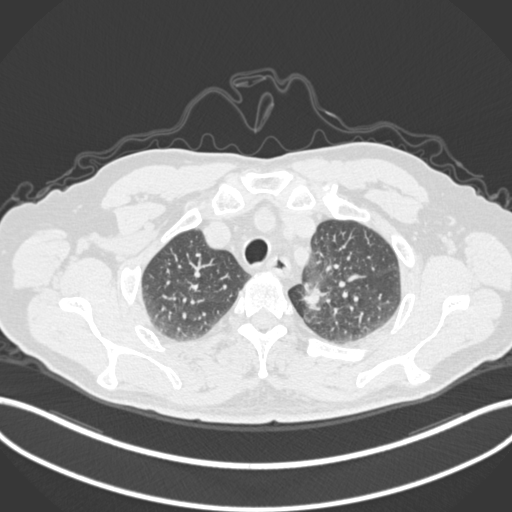
Chest CT, one axial slice; position 269 of 306 along the scan axis; reconstruction kernel B30f; 120 kVp; lung window (W 1500 / L -600 HU); 1 mm slice thickness; 512 × 512 image matrix, field of view 400 × 400 mm. Patient: male, 64 years. Case-level facts recorded for this patient, not image findings: clinical TNM (as recorded): T1c N0 M0.
Structures marked on this image (rectangle marked by the reading radiologist):
- lung tumour (recorded histology: adenocarcinoma): bounding box <300,277,332,314> (left, top, right, bottom; pixels)